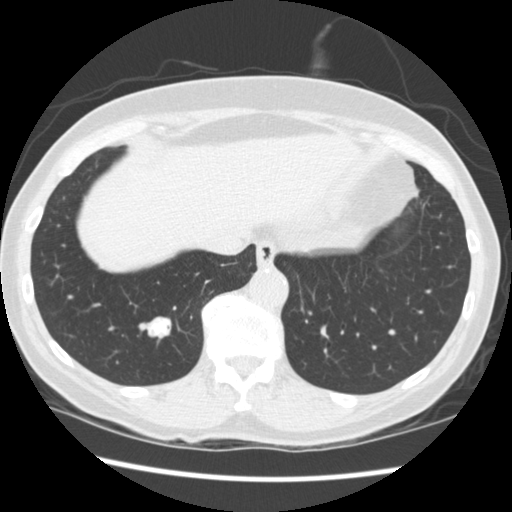
Low-dose screening chest CT, one axial slice. Slice 64 of 262 in the series (ordered by position). Lung window (W 1500 / L -600 HU). 2.5 mm slice thickness. 512 × 512 image matrix, field of view 340 × 340 mm.
Annotated regions visible in this slice (expert manual segmentation):
- lesion 1 (tumor, lower lobe of right lung): bounding box [x1, y1, x2, y2] px = [148, 317, 171, 338]